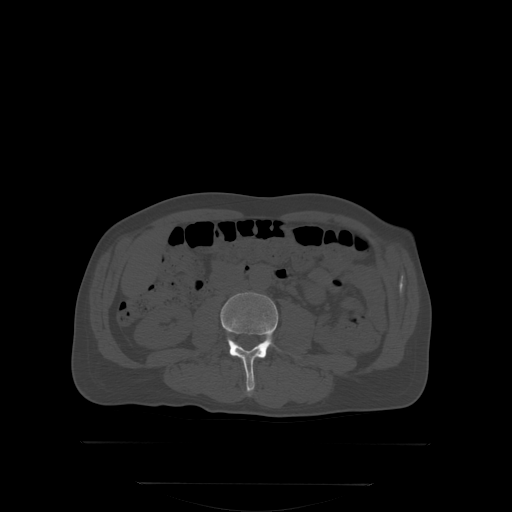
CT including the spine, one axial slice; position 121 of 350 along the scan axis; bone window (W 1800 / L 400 HU); 512 × 512 image matrix, field of view 500 × 500 mm. Patient: male, 58 years. From the clinical record (not read from this slice): primary cancer: prostate; vertebrae with lytic lesions (as recorded): L1.
Outlined on this slice (semi-automatically segmented with operator editing):
- L3 vertebra: bounding box (x1, y1, x2, y2) in pixels: (220, 292, 302, 394)